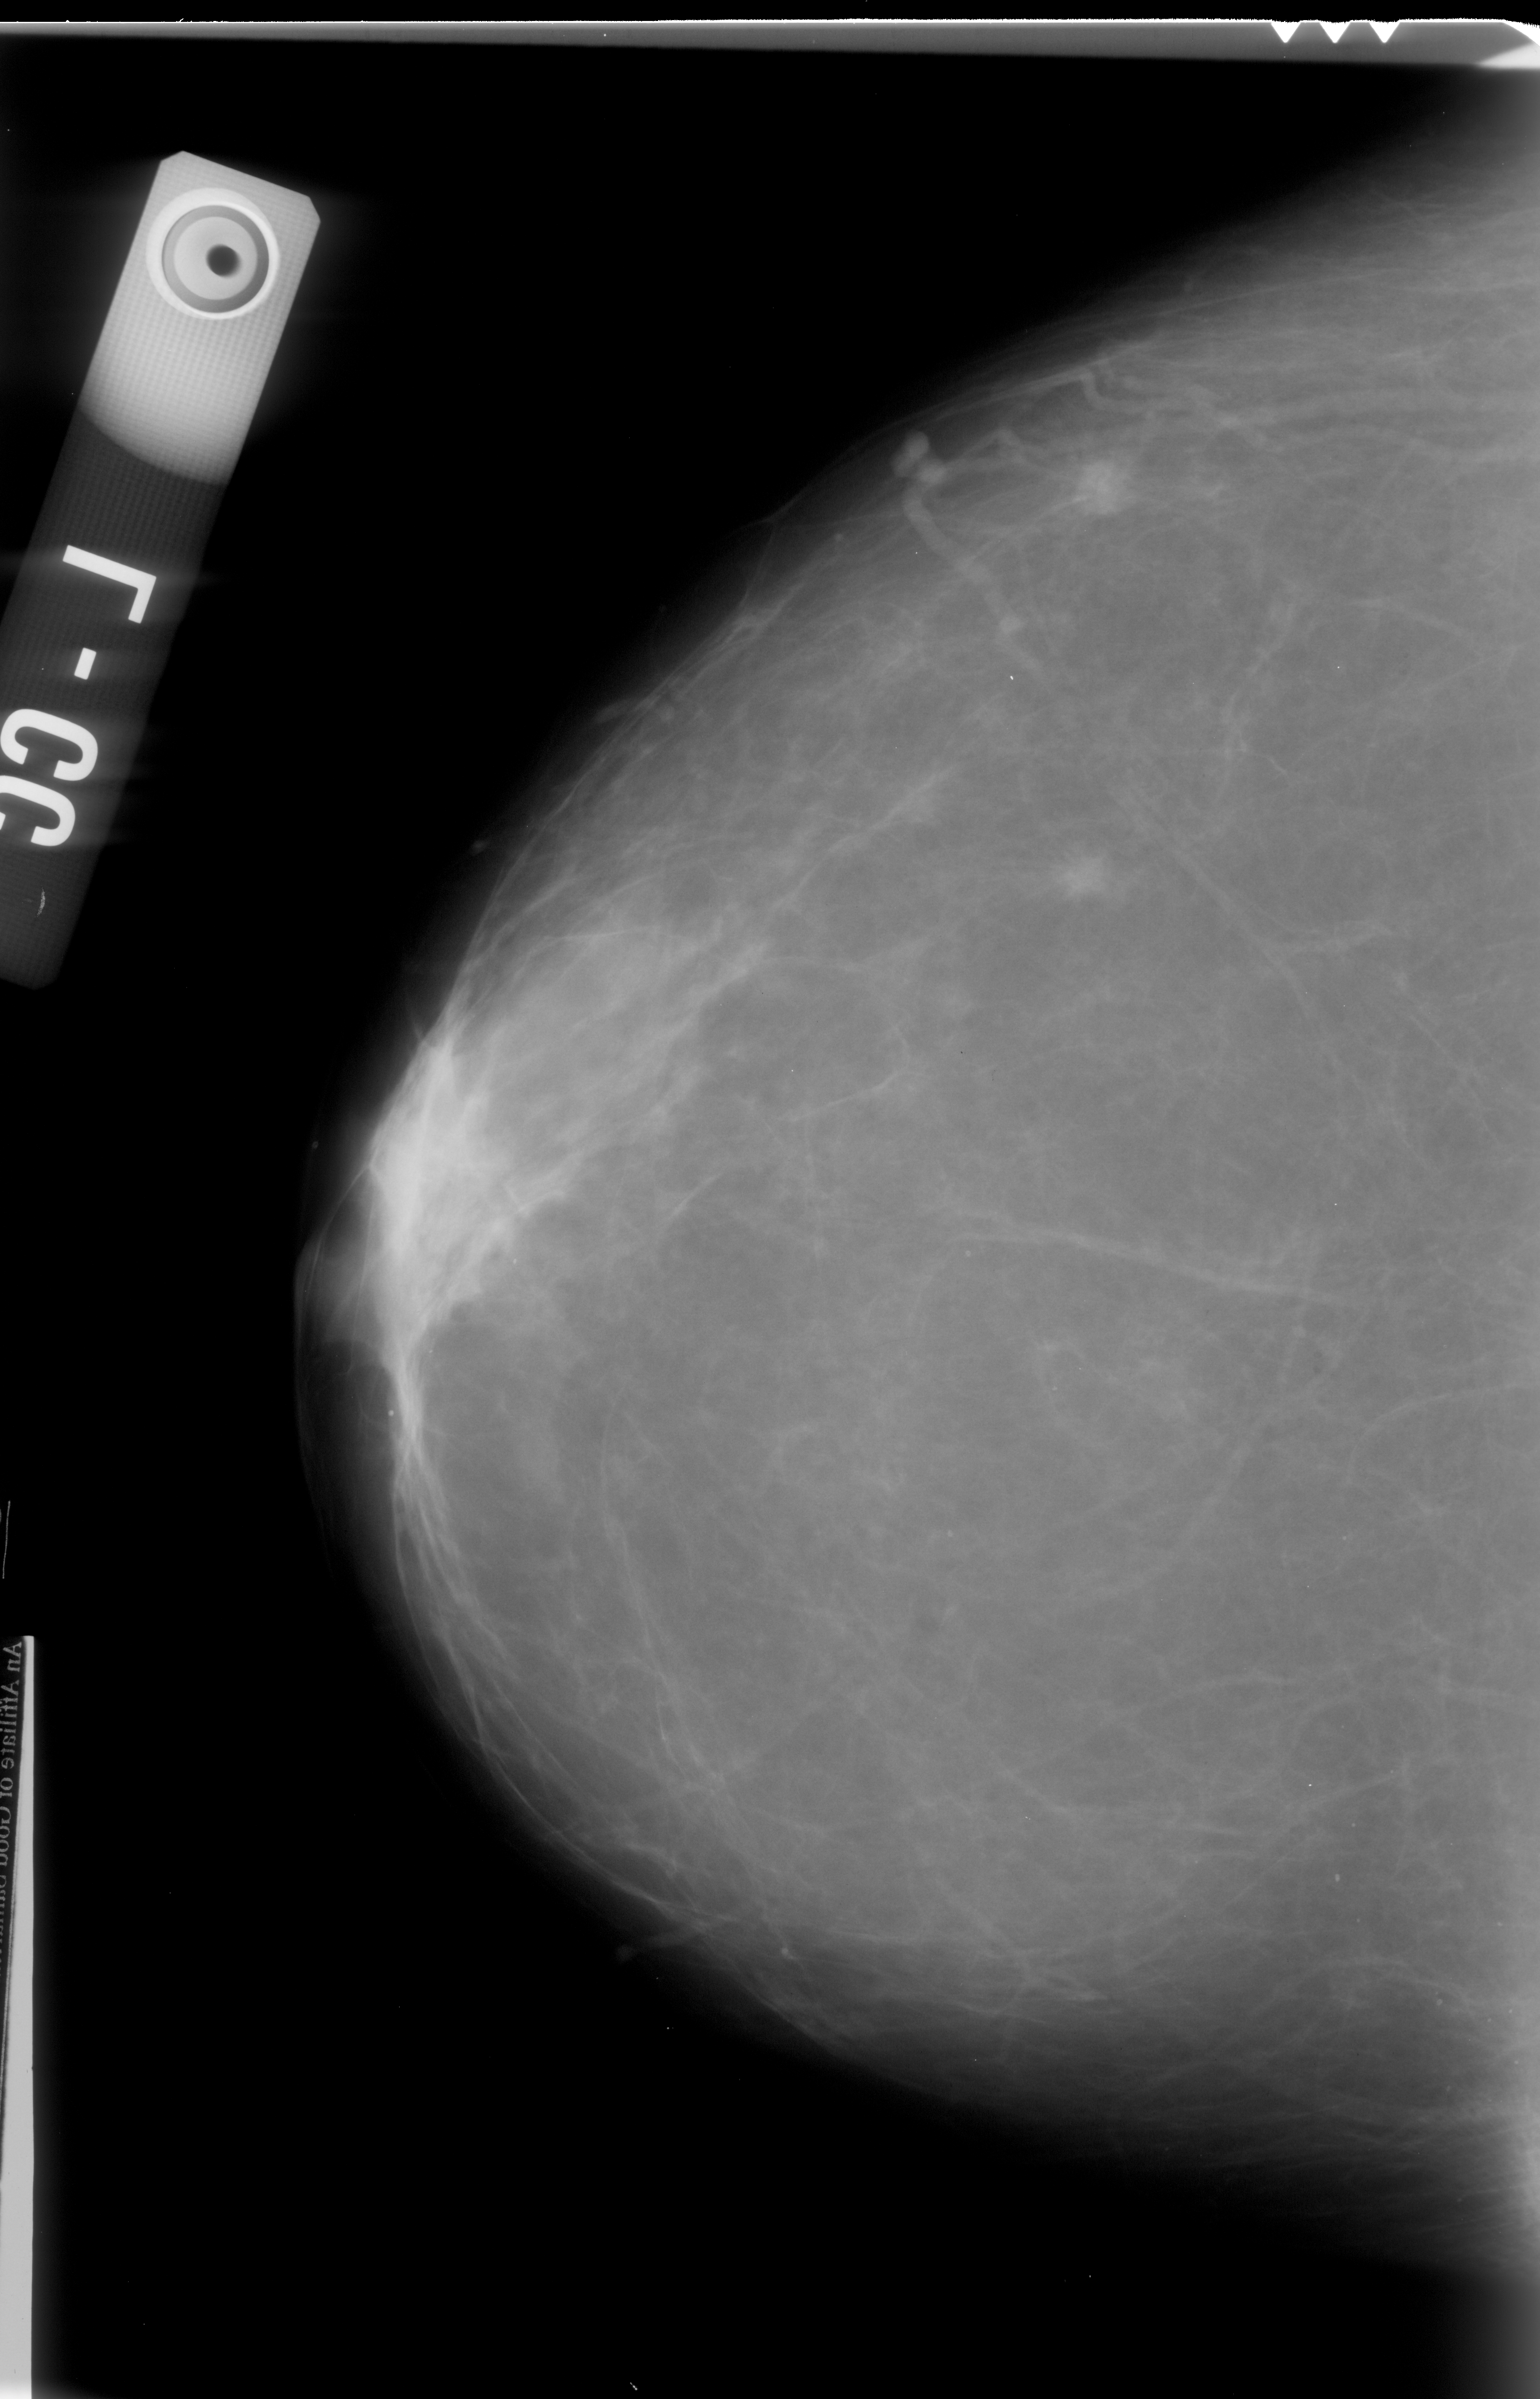
Digitized screen-film mammogram; left breast; CC view; BI-RADS breast density category 2 (scale 1–4); 1540 × 2399 image matrix.
Marked abnormalities (boxes around the expert regions of interest):
- mass, shape irregular, margins spiculated; BI-RADS assessment category 4; subtlety rating 1 on a 1 (subtle) to 5 (obvious) scale; pathology result (as recorded, not read from the image): malignant: bounding box (x1, y1, x2, y2) in pixels: (997, 838, 1118, 911)